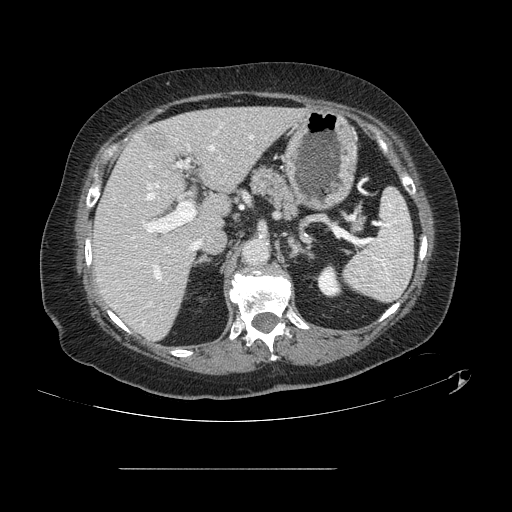
Contrast-enhanced abdominal CT, one axial slice; slice 77 of 148 in the series (ordered by position); 120 kVp; soft-tissue window (W 400 / L 40 HU); 512 × 512 image matrix, field of view 439 × 439 mm. Female patient, age 75 years. From the clinical record (not read from this slice): diagnosis: colorectal cancer liver metastases, imaged before liver resection.
Structures marked on this image (outlined manually by an expert reader):
- hepatic veins: bounding box <147,146,214,249> (left, top, right, bottom; pixels)
- liver: <93,108,301,340>
- planned liver remnant (the part of the liver to remain after resection): <93,108,301,340>
- portal vein (with intrahepatic branches): <132,133,254,279>
- liver metastasis: <142,131,168,148>